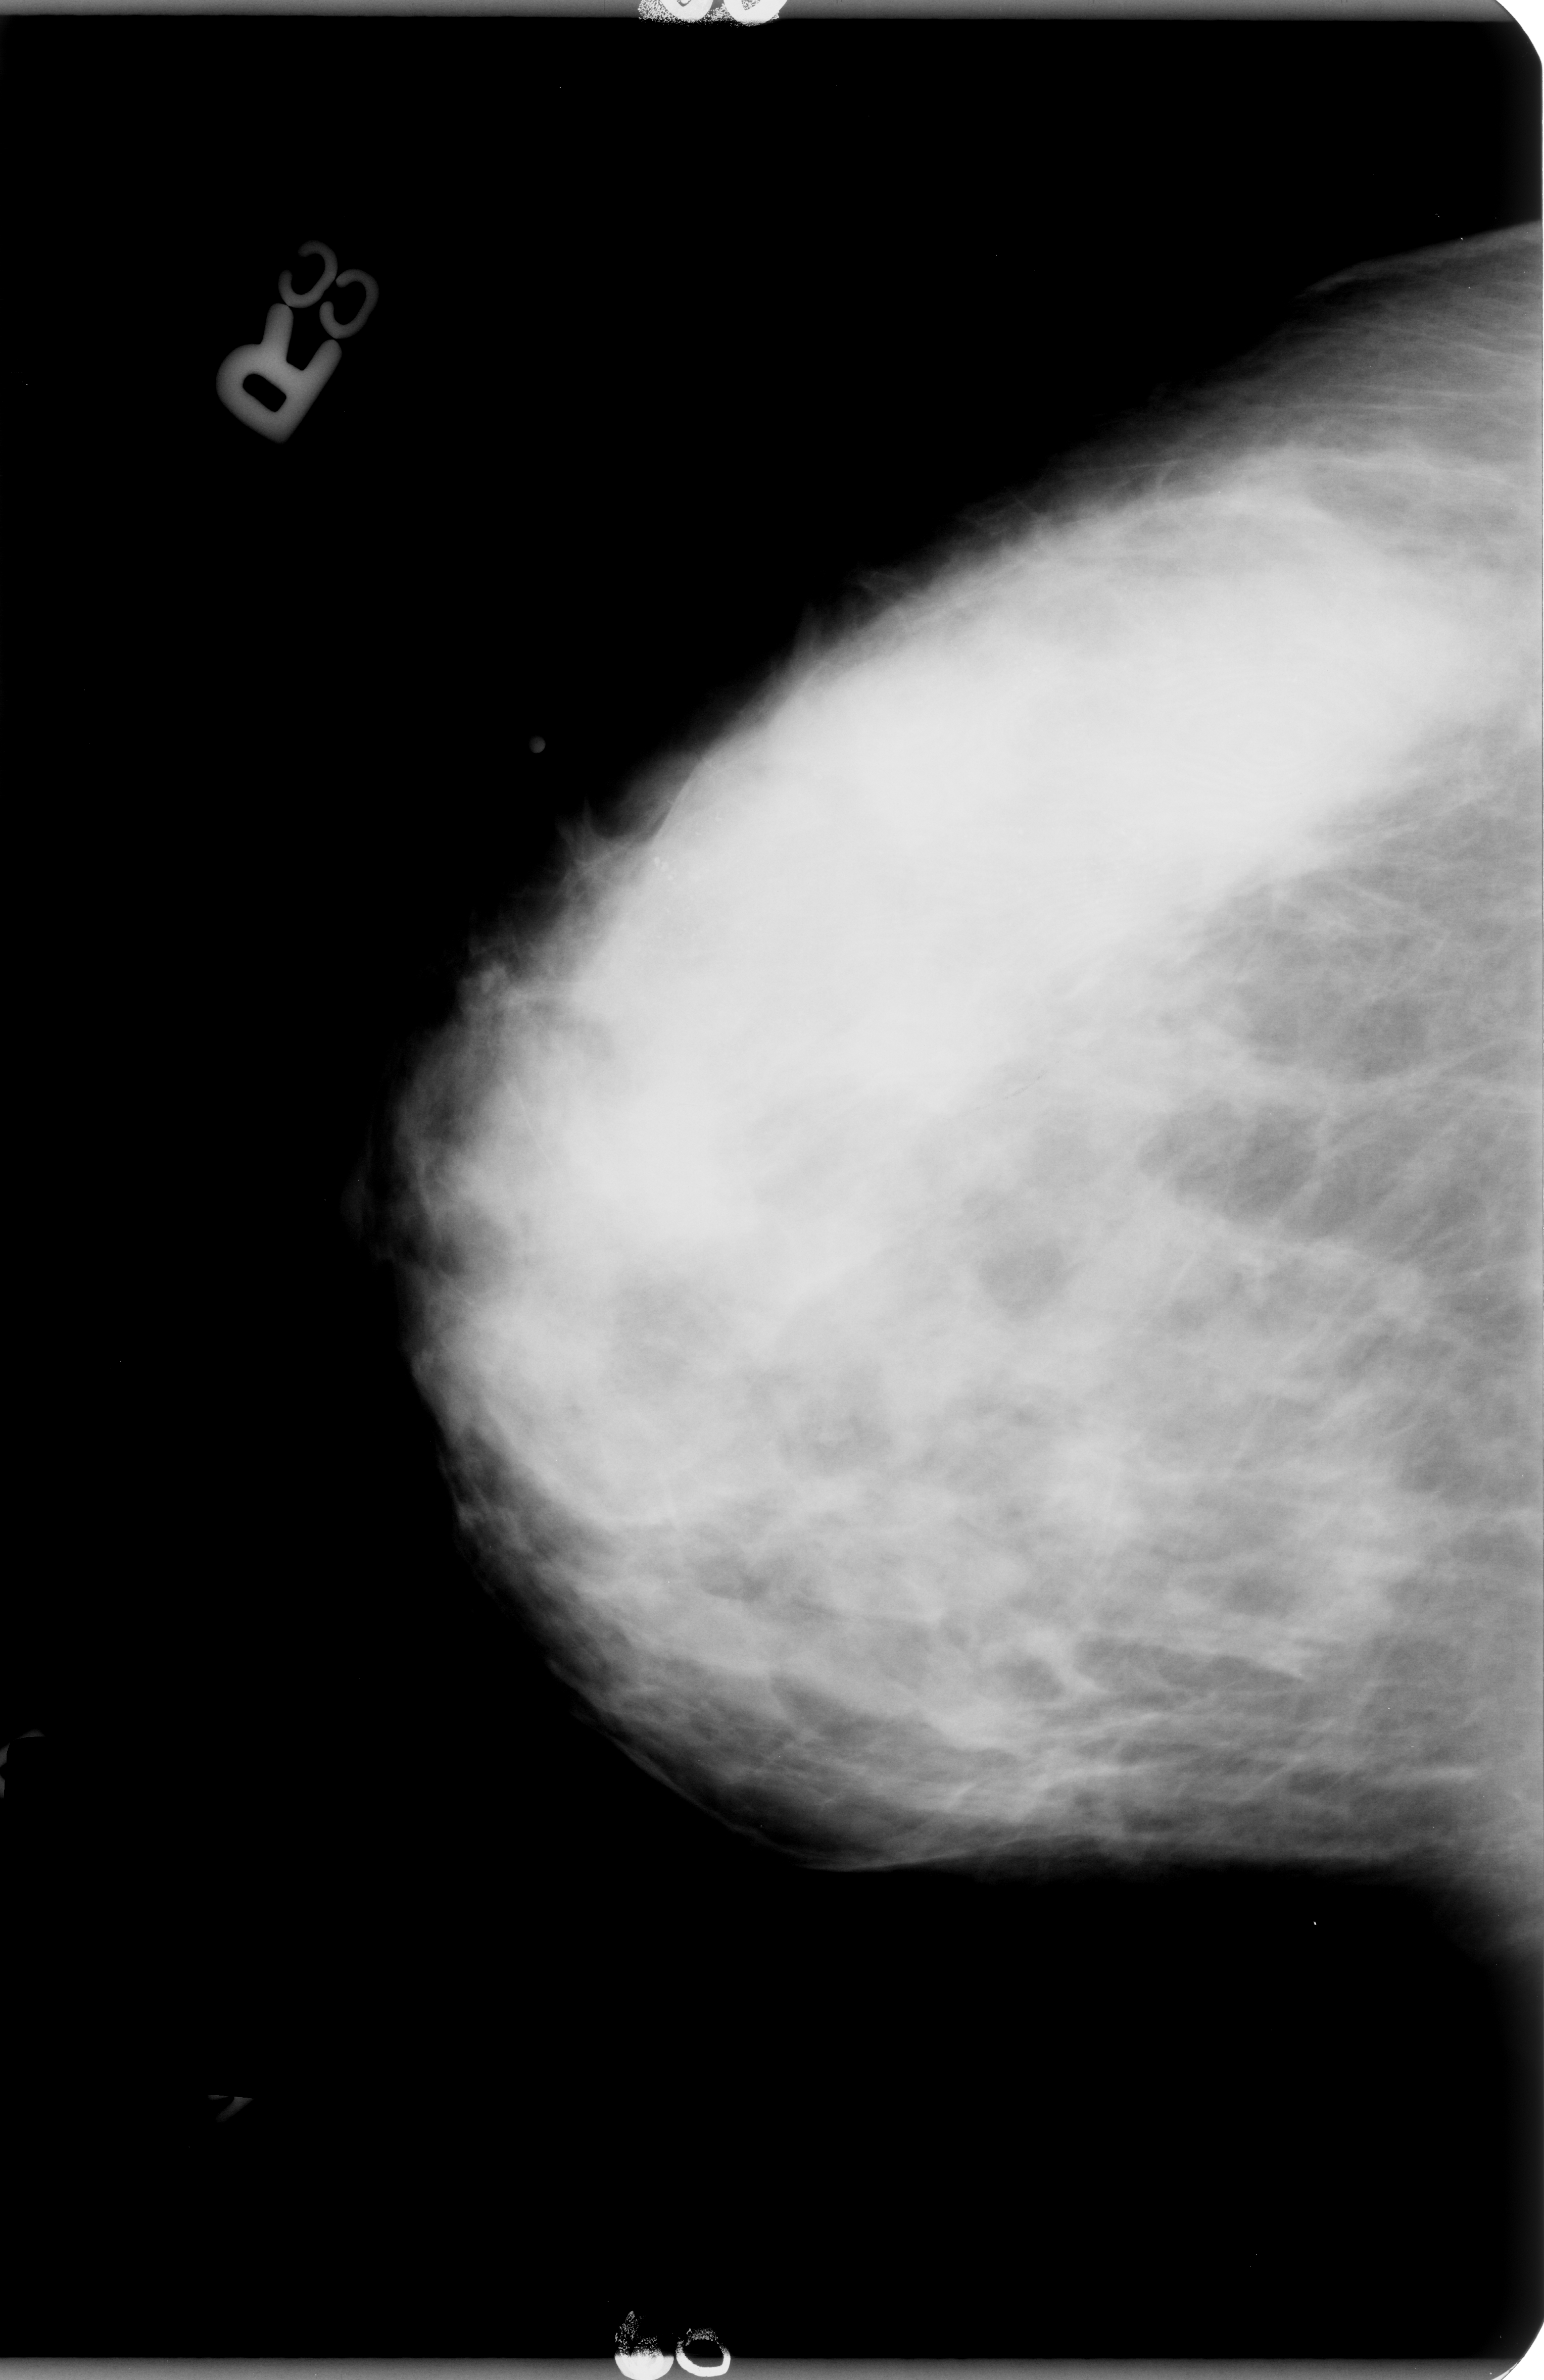
Mammogram (digitized film). Right breast. Craniocaudal (CC) view. BI-RADS breast density category 3 (scale 1–4). 1544 × 2380 image matrix.
Expert-marked regions of interest on this image (one box per marked abnormality):
- calcifications, morphology pleomorphic, distribution regional; BI-RADS assessment category 4; pathology result (as recorded, not read from the image): malignant: bounding box (x1, y1, x2, y2) in pixels: (505, 492, 1488, 1140)